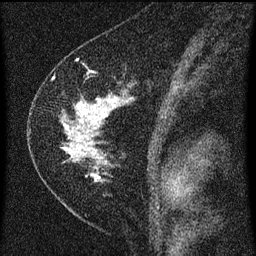
Breast MRI (dynamic contrast-enhanced), one sagittal slice; slice 38 of 60 in the series (ordered by position); dynamic contrast-enhanced series, image 2 of 3 at this slice position (ordered by acquisition); 1.5 T; TE 4.2 ms, TR 8 ms; 2 mm slice thickness; 256 × 256 image matrix, field of view 180 × 180 mm. Female patient, age 47 years.
Annotated regions visible in this slice (semi-automatic segmentation, software-assisted and operator-edited):
- analysis volume of interest (the breast-tissue region the enhancement analysis was run in; not a lesion): bounding box (x1, y1, x2, y2) in pixels: (38, 78, 132, 191)
- tumour enhancement mask (voxels above the 70 % enhancement threshold inside the analysis volume of interest): (63, 98, 120, 183)